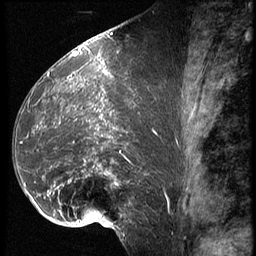
Breast MRI (dynamic contrast-enhanced), one sagittal slice; position 32 of 62 along the scan axis; 3 images stored at this slice position (order not interpretable as contrast timing); 1.5 T; TE 4.2 ms, TR 9 ms; 2.5 mm slice thickness; 256 × 256 image matrix. Patient: female, 39 years. From the clinical record (not read from this slice): setting: breast cancer imaged before/during neoadjuvant chemotherapy; receptor status: HER2-positive.
Outlined on this slice (semi-automatically segmented with operator editing):
- analysis volume of interest (the breast-tissue region the enhancement analysis was run in; not a lesion): bounding box <16,64,166,228> (left, top, right, bottom; pixels)
- tumour enhancement mask (voxels above the 140 % enhancement threshold inside the analysis volume of interest): <33,79,161,214>